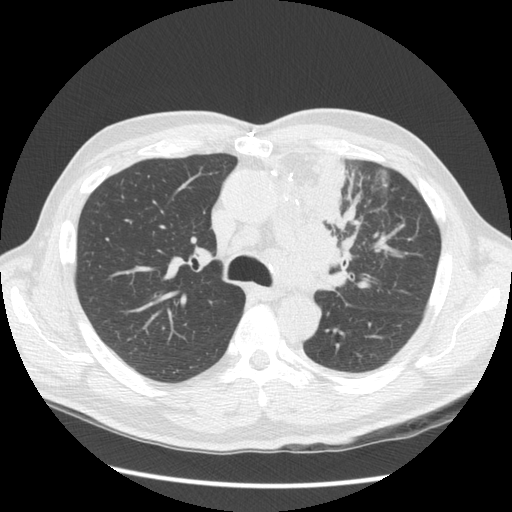
Low-dose screening chest CT, one axial slice. Slice 93 of 136 in the series (ordered by position). 120 kVp. Lung window (W 1500 / L -600 HU). 2.5 mm slice thickness. 512 × 512 image matrix, field of view 360 × 360 mm.
Structures marked on this image (expert manual segmentation):
- lesion 1 (tumor, upper lobe of left lung): bounding box [x1, y1, x2, y2] px = [299, 152, 348, 295]